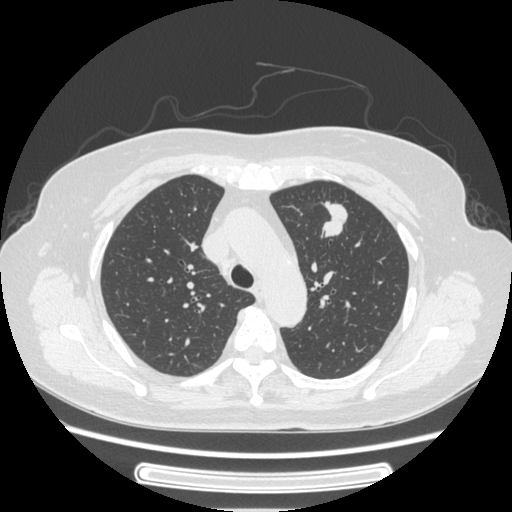
Chest CT, one axial slice; slice 174 of 227 in the series (ordered by position); 120 kVp; lung window (W 1500 / L -600 HU); 512 × 512 image matrix, field of view 363 × 363 mm. Female patient, age 77 years. From the clinical record (not read from this slice): clinical TNM (as recorded): T1c N3 M0; histopathological grade: G2-3.
Outlined on this slice (bounding box drawn by a radiologist):
- lung tumour (recorded histology: adenocarcinoma): bounding box (x1, y1, x2, y2) in pixels: (314, 195, 361, 251)